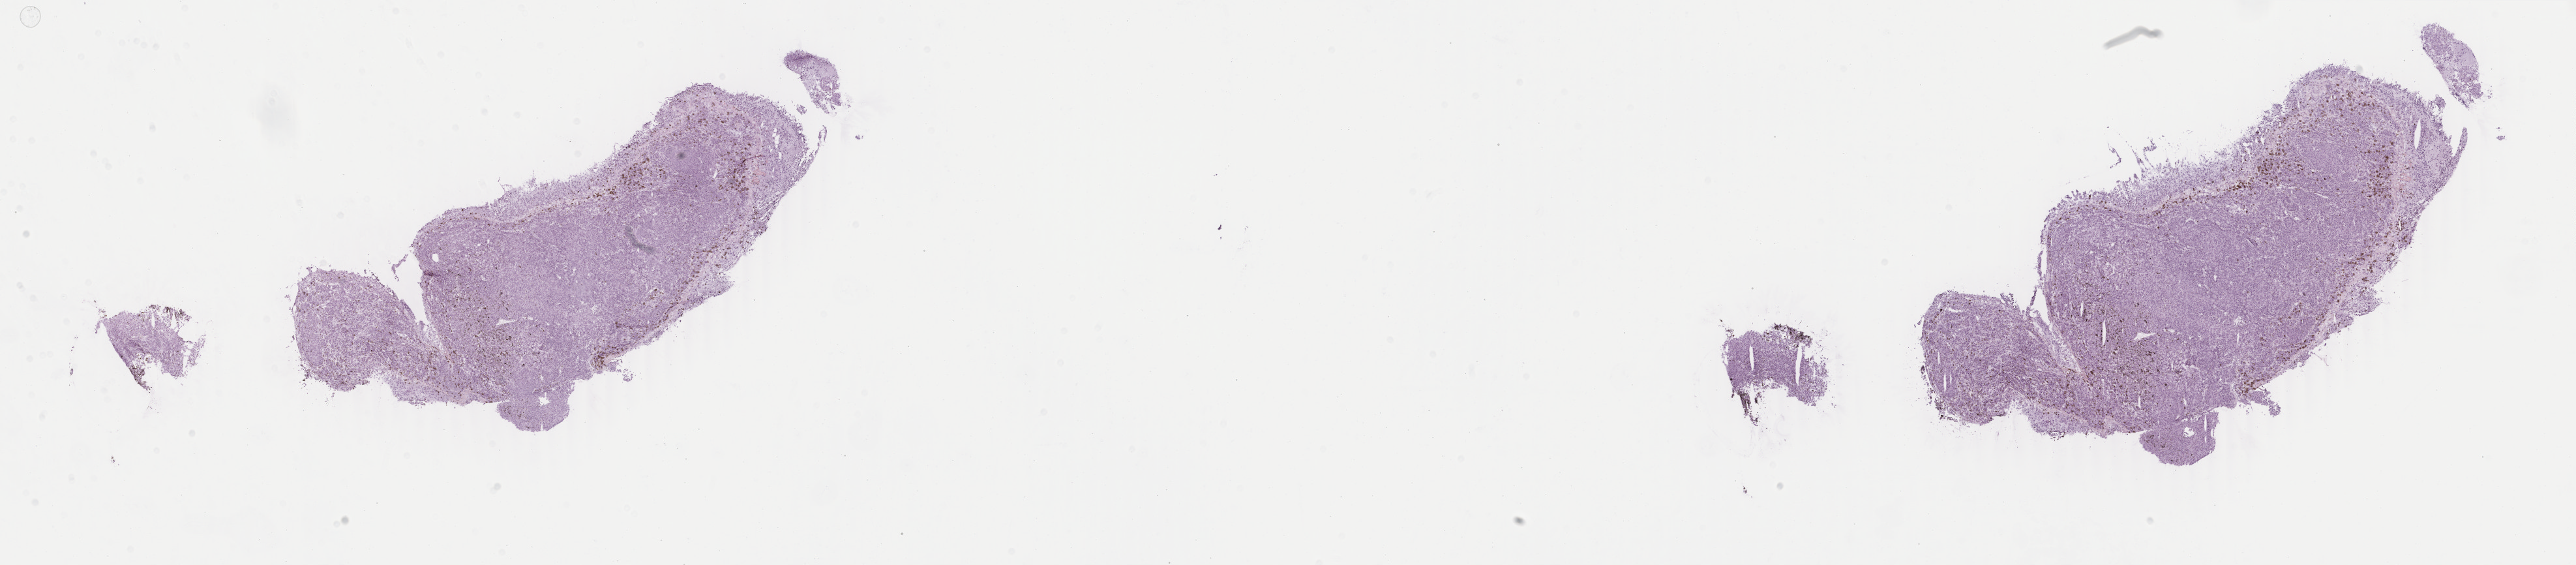
H&E-stained whole-slide image — shown as a low-resolution overview of the whole scanned area (about 31.4 x 6.9 mm, acquisition: 40x scan); frozen section; primary tumour sample from the uvea. Female, age 55 years at initial diagnosis. Pathologist review of this section (percent, as recorded): tumour cells 90%, tumour nuclei 90%, normal cells 10%, stromal cells 0%, necrosis 0%. Infiltration values recorded for this section: lymphocyte infiltration 0%, monocyte infiltration 0%, neutrophil infiltration 0%.
AJCC pathologic stage: IIIA (7th edition). Pathologic diagnosis: Epithelioid cell melanoma (choroid).